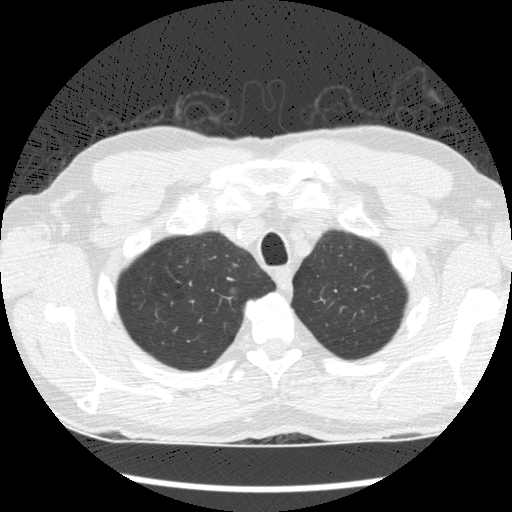
Low-dose screening chest CT, one axial slice. Position 139 of 164 along the scan axis. Lung window (W 1500 / L -600 HU). 2.5 mm slice thickness. 512 × 512 image matrix, field of view 340 × 340 mm.
Structures marked on this image (expert manual segmentation):
- lesion 1 (tumor, upper lobe of right lung): bounding box [x1, y1, x2, y2] px = [229, 286, 238, 294]